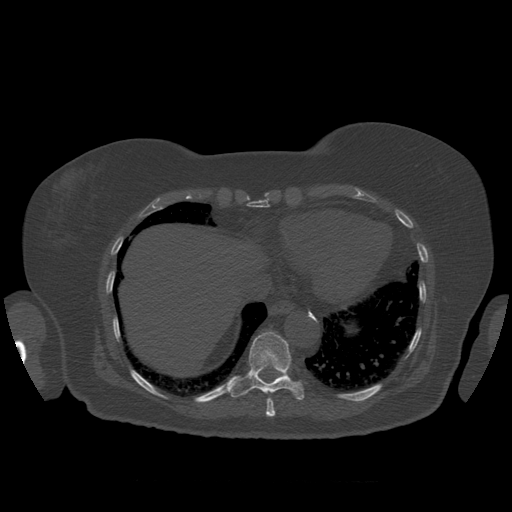
CT including the spine, one axial slice; position 343 of 399 along the scan axis; reconstruction kernel STANDARD; 120 kVp; bone window (W 1800 / L 400 HU); 1.25 mm slice thickness; 512 × 512 image matrix, field of view 404 × 404 mm. Patient age 81 years. From the clinical record (not read from this slice): primary cancer: renal; vertebrae with lytic lesions (as recorded): L1.
Outlined on this slice (semi-automatic segmentation, software-assisted and operator-edited):
- T10 vertebra: box from (x=232, y=332) to (x=305, y=400) px
- T9 vertebra: (x=266, y=398)–(x=276, y=417)